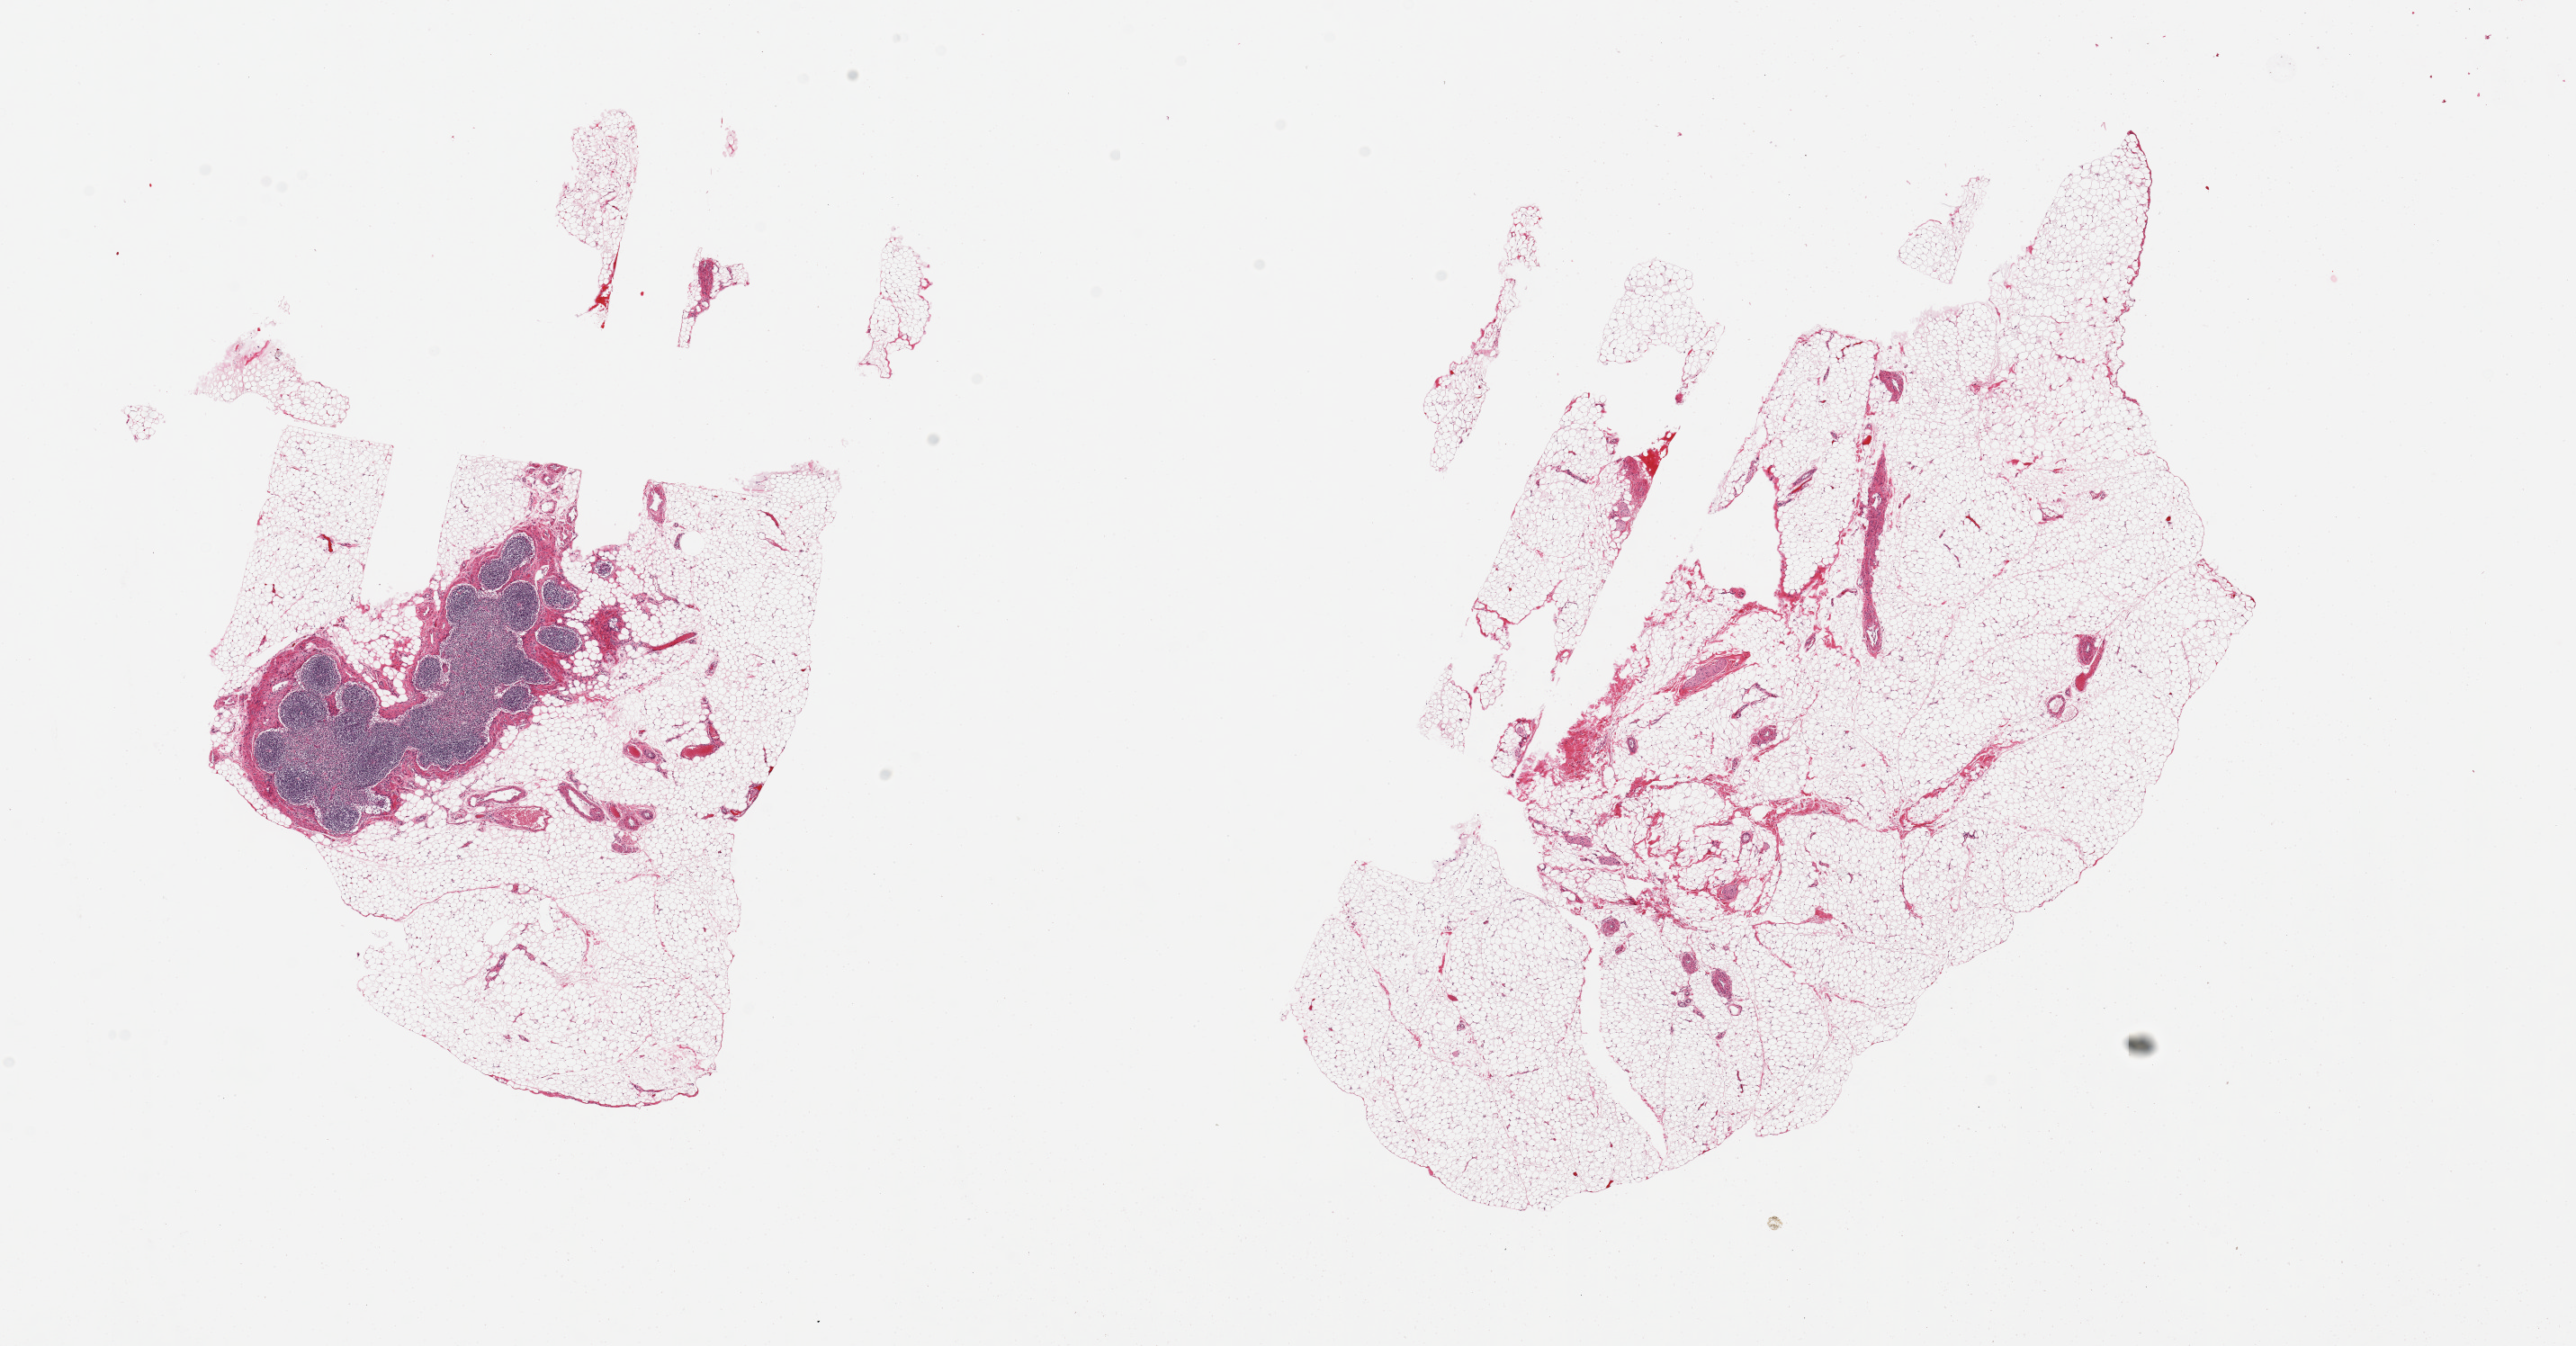
Haematoxylin and eosin whole-slide image, brightfield — low-resolution overview of the scanned area, about 22.6 x 11.8 mm. PAXgene-fixed paraffin-embedded (PFPE) section. Section of omentum (target tissue). Donor tissue sample. Female donor.
• reviewer comment on this tissue sample: 2 pieces, incidentaly ~3mm lymph node in one section; ~10% vessel/fibrous interstitial tissue